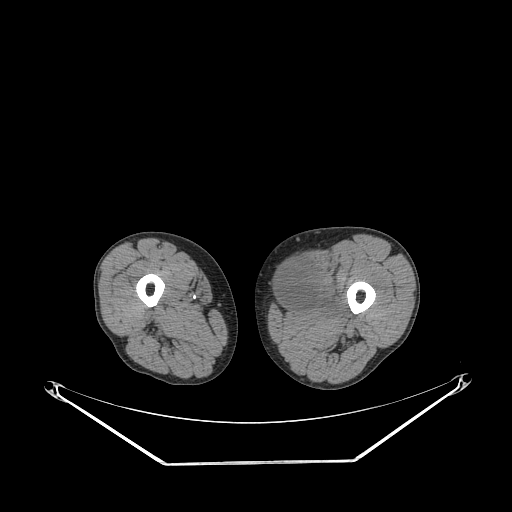
CT of an extremity soft-tissue mass (from a PET/CT study), one axial slice; position 229 of 267 along the scan axis; soft-tissue window (W 400 / L 40 HU); 512 × 512 image matrix, field of view 500 × 500 mm. Male patient. Case-level facts recorded for this patient, not image findings: histological type: pleiomorphic liposarcoma; grade: high; site of the primary tumour: left thigh.
Annotated regions visible in this slice (expert contour drawn on MRI and transferred to this co-registered scan by the dataset authors):
- gross tumour volume including surrounding oedema: bounding box [x1, y1, x2, y2] px = [276, 258, 344, 318]
- gross tumour volume (mass): [276, 257, 320, 307]